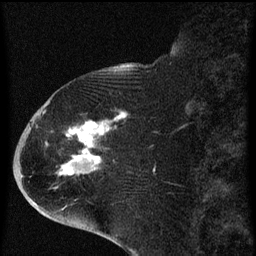
Breast MRI (dynamic contrast-enhanced), one sagittal slice; slice 24 of 60 in the series (ordered by position); dynamic contrast-enhanced series, image 2 of 4 at this slice position (ordered by acquisition); 1.5 T; TE 4.2 ms, TR 8 ms; 256 × 256 image matrix. Female patient, age 71 years.
Structures marked on this image (semi-automatic segmentation, software-assisted and operator-edited):
- analysis volume of interest (the breast-tissue region the enhancement analysis was run in; not a lesion): bounding box <32,86,130,205> (left, top, right, bottom; pixels)
- tumour enhancement mask (voxels above the 70 % enhancement threshold inside the analysis volume of interest): <43,112,128,175>